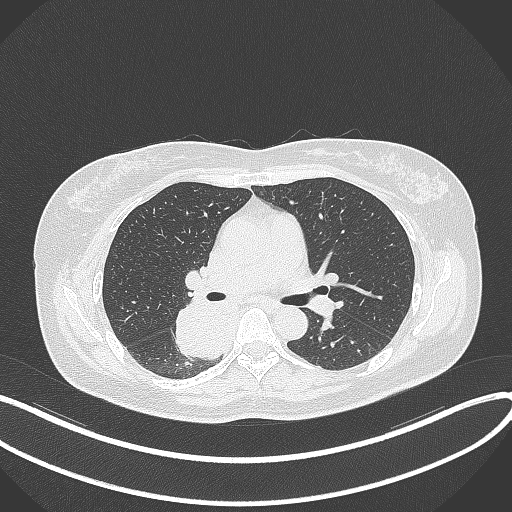
Chest CT, one axial slice; position 213 of 331 along the scan axis; 120 kVp; lung window (W 1500 / L -600 HU); 512 × 512 image matrix, field of view 400 × 400 mm. Patient: female, 54 years. From the clinical record (not read from this slice): clinical TNM (as recorded): T4 N0 M0.
Annotated regions visible in this slice (bounding box drawn by a radiologist):
- lung tumour (recorded histology: adenocarcinoma): bounding box (x1, y1, x2, y2) in pixels: (169, 302, 234, 368)